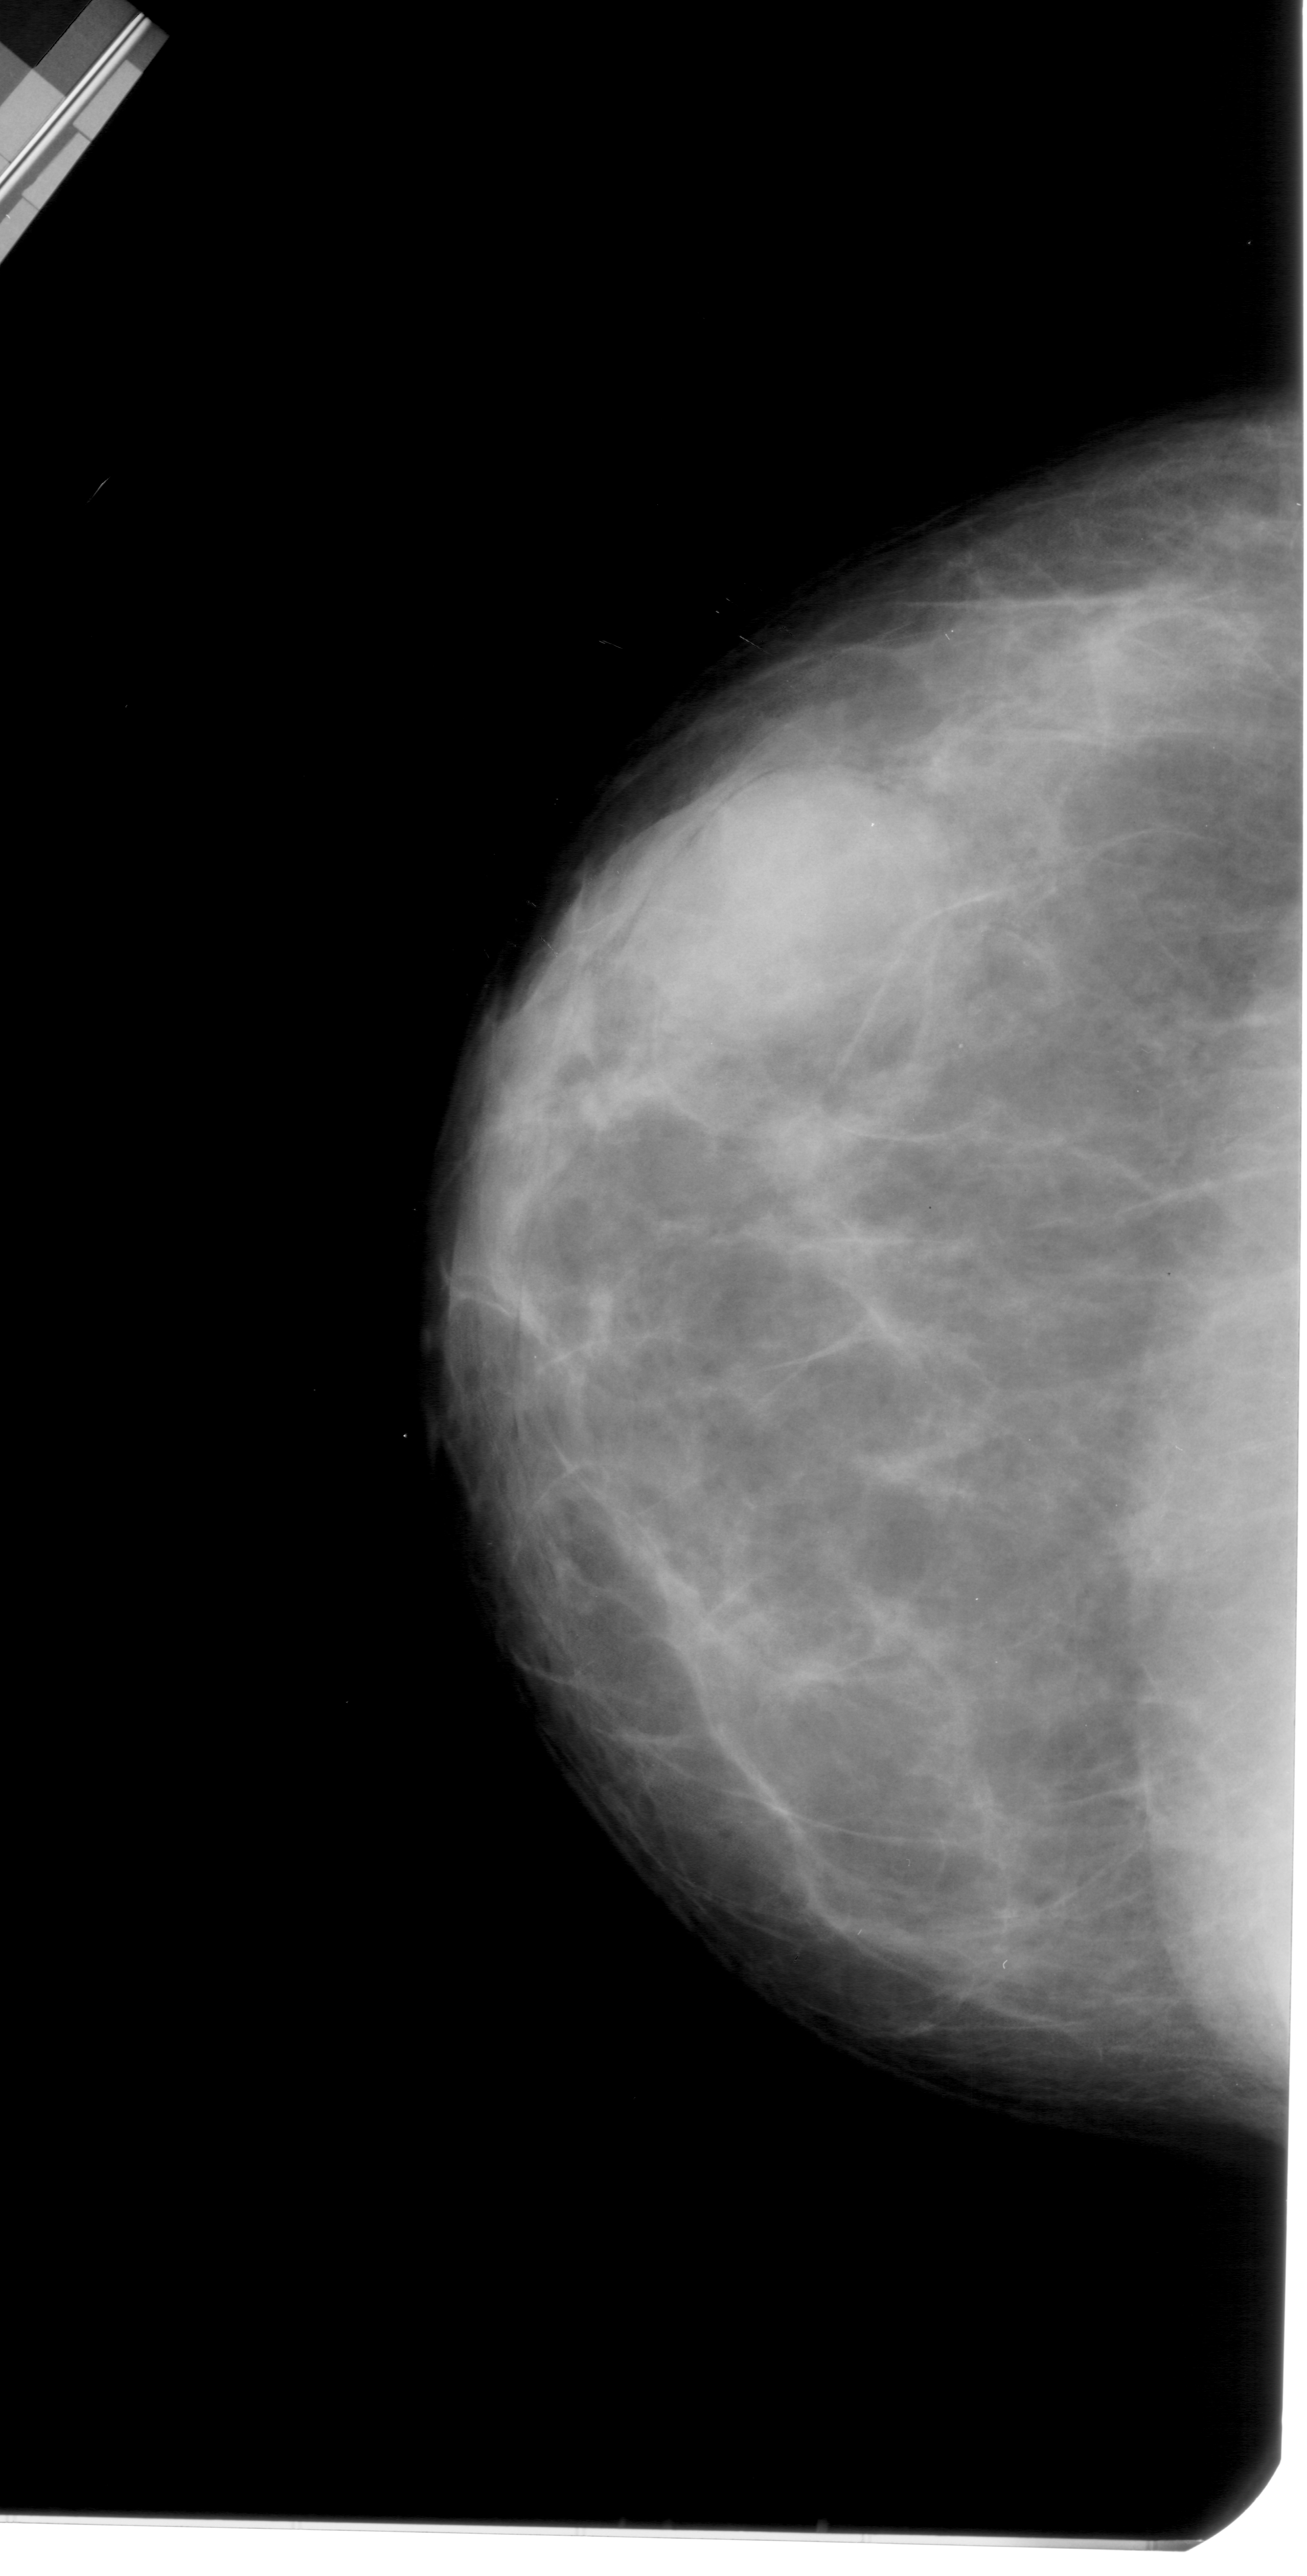
Mammogram (digitized film), left breast, craniocaudal (CC) view, BI-RADS breast density category 4 (scale 1–4).
Mass, shape oval, margins obscured; BI-RADS assessment category 4; pathology (as recorded): benign.